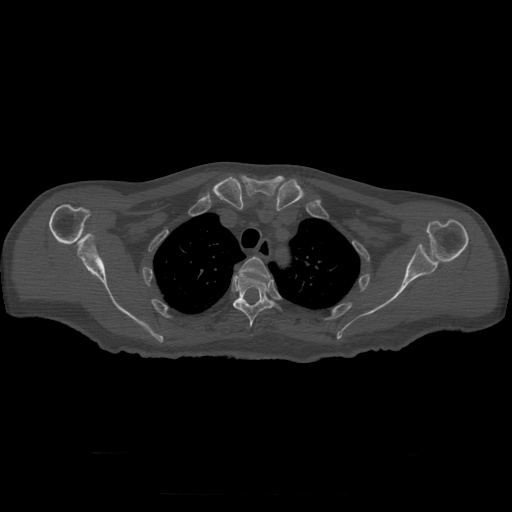
CT including the spine, one axial slice. Slice 244 of 397 in the series (ordered by position). Reconstruction kernel STANDARD. 120 kVp. Bone window (W 1800 / L 400 HU). 512 × 512 image matrix, field of view 510 × 510 mm. Patient age 73 years. From the clinical record (not read from this slice): primary cancer: prostate.
Outlined on this slice (semi-automatically segmented with operator editing):
- T3 vertebra: bounding box [x1, y1, x2, y2] px = [240, 257, 270, 278]
- T4 vertebra: [233, 274, 275, 328]
- T5 vertebra: [233, 299, 238, 305]